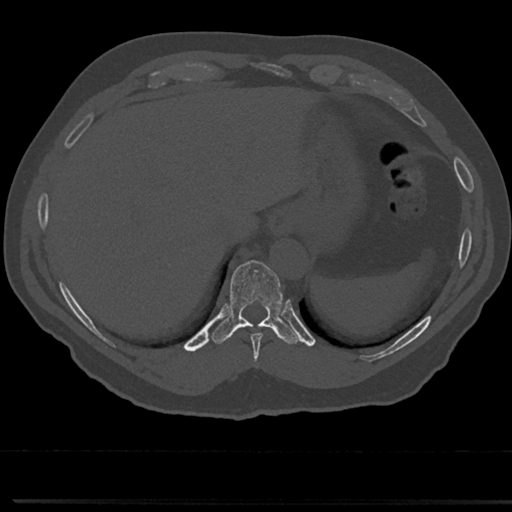
CT including the spine, one axial slice. Position 269 of 817 along the scan axis. Reconstruction kernel Br40s/3. 120 kVp. Bone window (W 1800 / L 400 HU). 512 × 512 image matrix. Patient: male, 61 years. From the clinical record (not read from this slice): primary cancer: prostate.
Outlined on this slice (semi-automatically segmented with operator editing):
- T10 vertebra: box from (x=229, y=261) to (x=282, y=324) px
- T9 vertebra: (x=237, y=322)–(x=279, y=353)